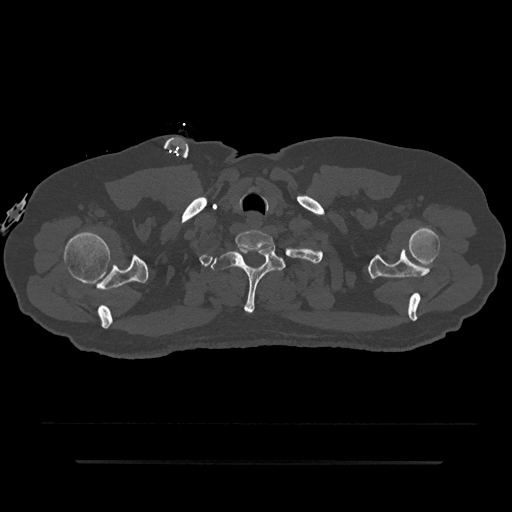
CT including the spine, one axial slice; slice 745 of 797 in the series (ordered by position); reconstruction kernel Br40s/3; bone window (W 1800 / L 400 HU); 0.5 mm slice thickness; 512 × 512 image matrix. Patient: male, 59 years. From the clinical record (not read from this slice): primary cancer: bile ducts; vertebrae with lytic lesions (as recorded): T10.
Annotated regions visible in this slice (semi-automatic segmentation, software-assisted and operator-edited):
- T1 vertebra: bounding box [x1, y1, x2, y2] px = [211, 247, 285, 314]